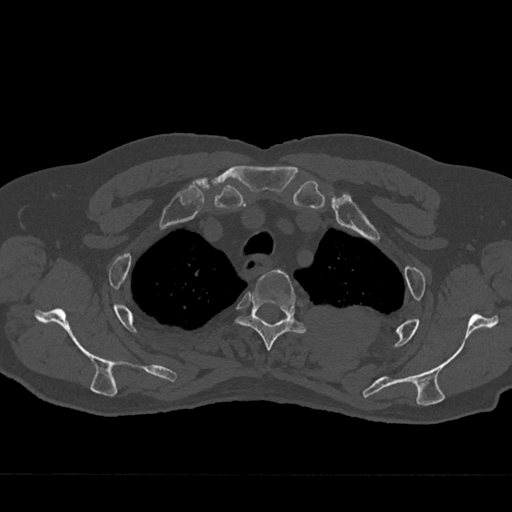
CT including the spine, one axial slice; slice 569 of 797 in the series (ordered by position); reconstruction kernel Br40s/3; 120 kVp; bone window (W 1800 / L 400 HU); 512 × 512 image matrix, field of view 377 × 377 mm. Male patient, age 75 years. From the clinical record (not read from this slice): primary cancer: renal; vertebrae with lytic lesions (as recorded): T4.
Structures marked on this image (semi-automatic segmentation, software-assisted and operator-edited):
- T3 vertebra: bounding box [x1, y1, x2, y2] px = [236, 269, 306, 351]